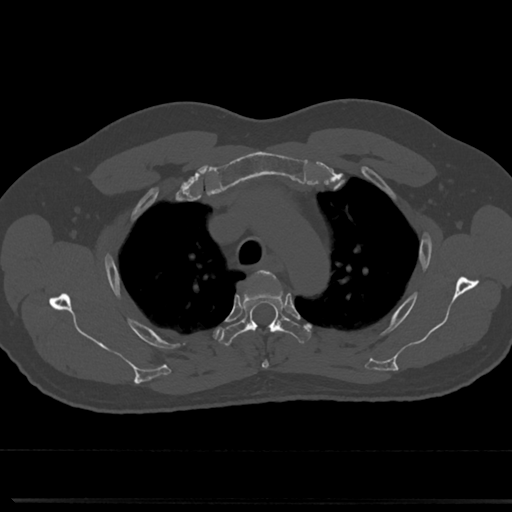
CT including the spine, one axial slice; position 560 of 817 along the scan axis; reconstruction kernel Br40s/3; 120 kVp; bone window (W 1800 / L 400 HU); 0.5 mm slice thickness; 512 × 512 image matrix, field of view 355 × 355 mm. Male patient, age 61 years. From the clinical record (not read from this slice): primary cancer: prostate.
Annotated regions visible in this slice (semi-automatically segmented with operator editing):
- T3 vertebra: bounding box <255,271,269,368> (left, top, right, bottom; pixels)
- T4 vertebra: <219,272,311,345>